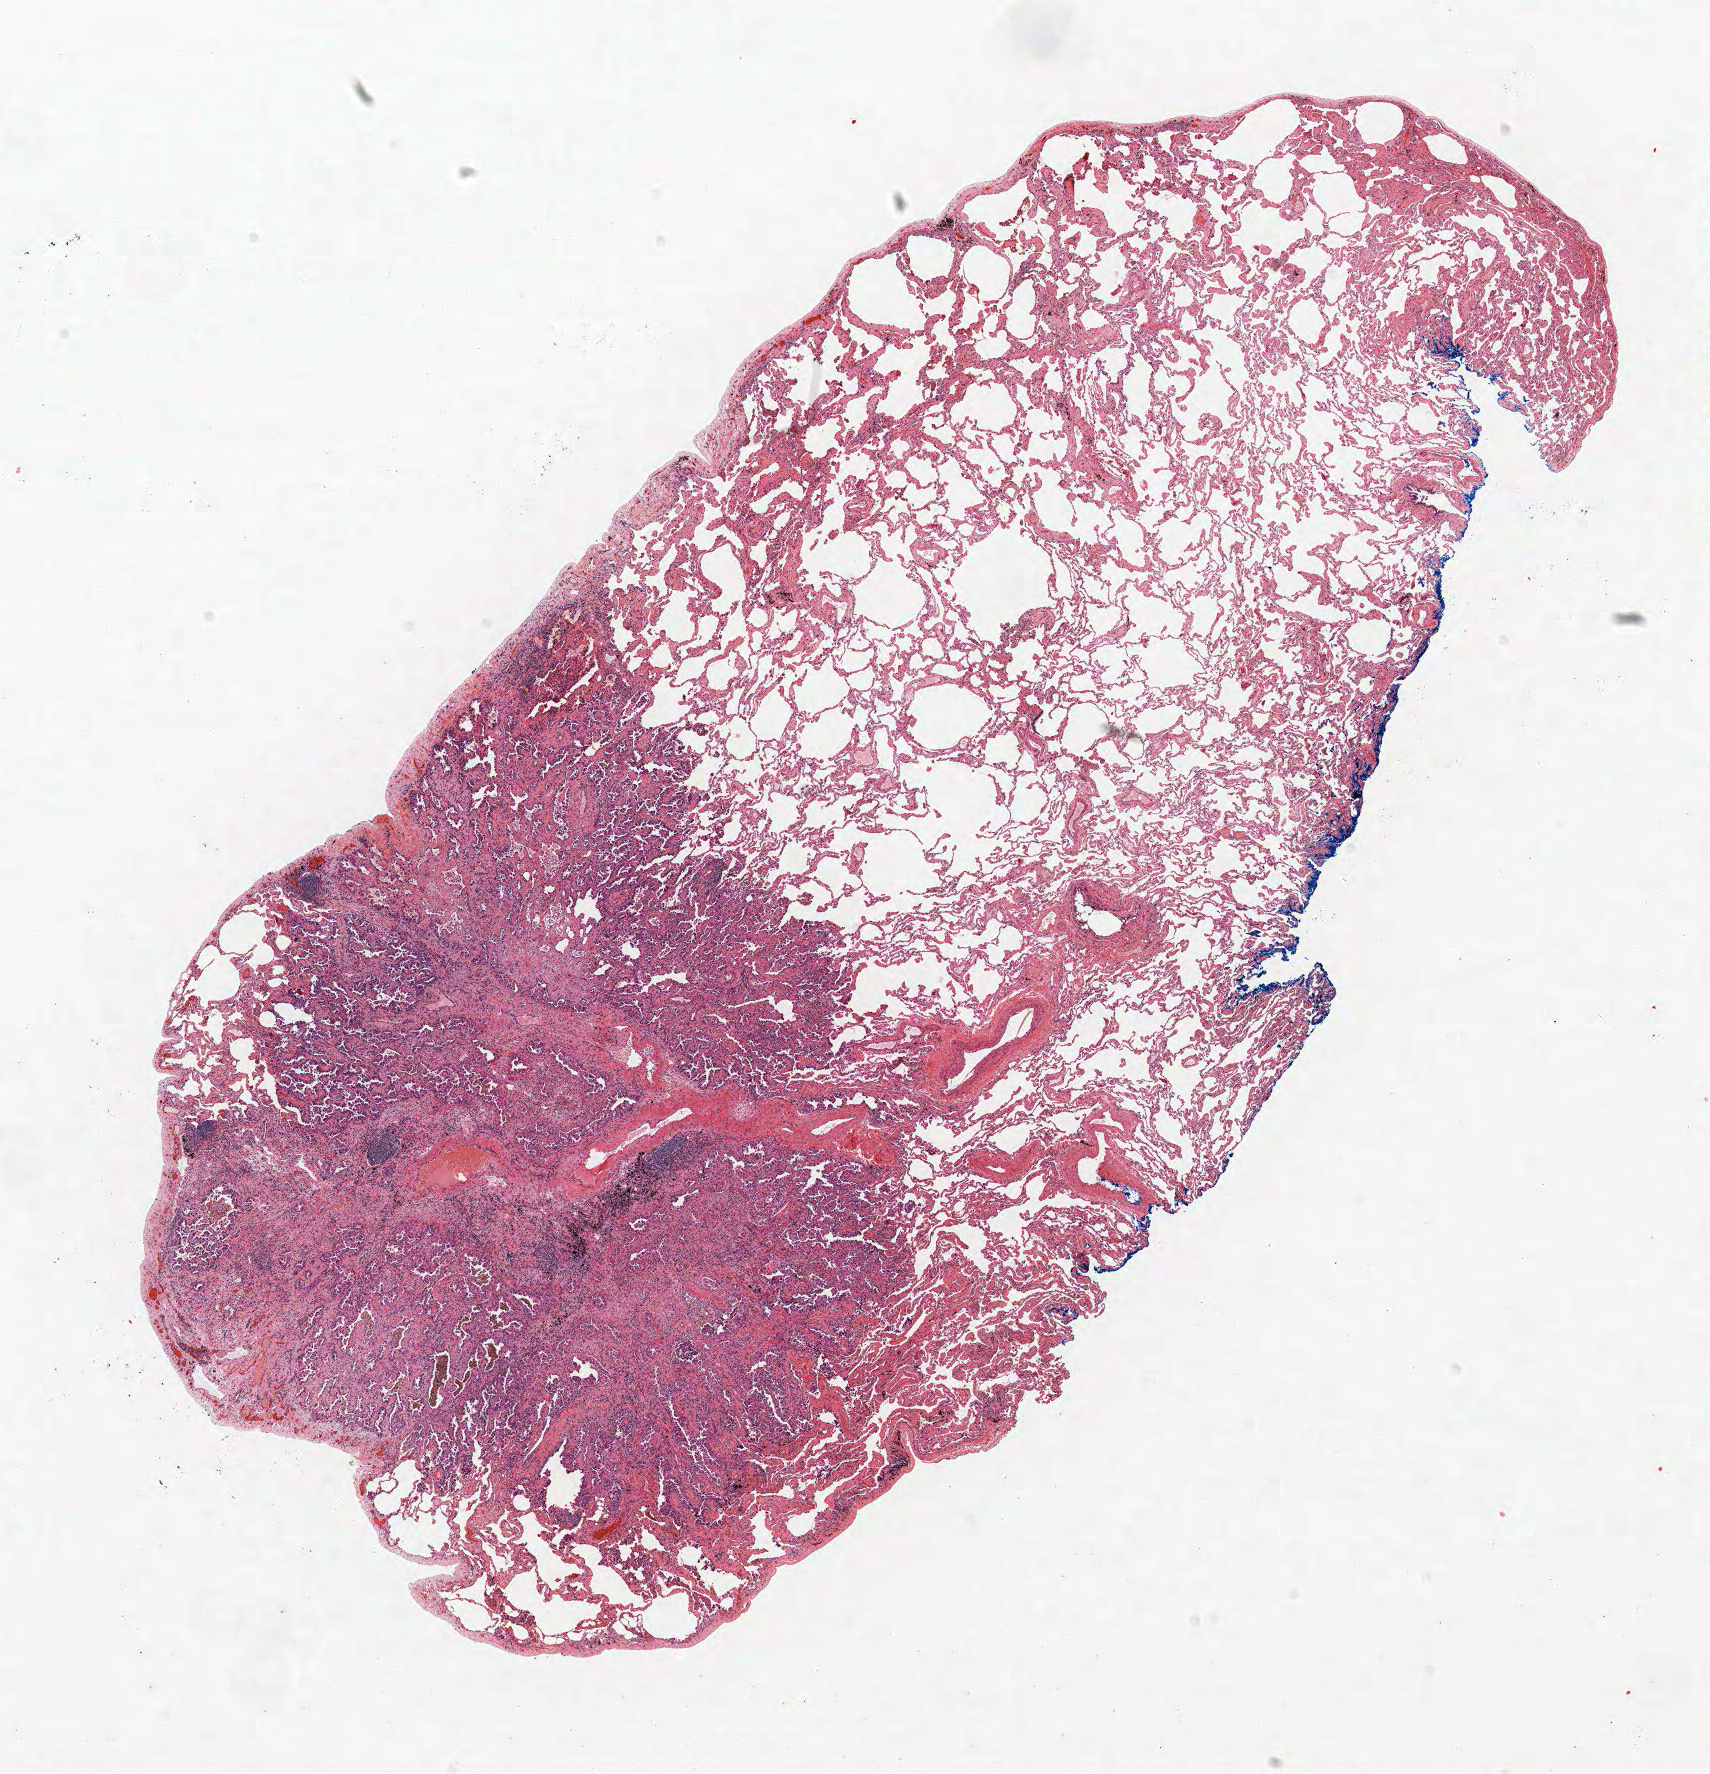
H&E whole-slide image, shown as a low-resolution overview of the whole scanned area (about 13.7 x 14.2 mm), formalin-fixed paraffin-embedded (FFPE) section, lung. Female patient, aged 61 at enrolment. Current smoker at enrolment. Grade: moderately differentiated (G2).
* primary tumour location (clinical record): right upper lobe
* stage (AJCC 6th edition): IA
* tumour size (pathology): 8 mm
* participant's lung-cancer diagnosis: Adenocarcinoma, NOS